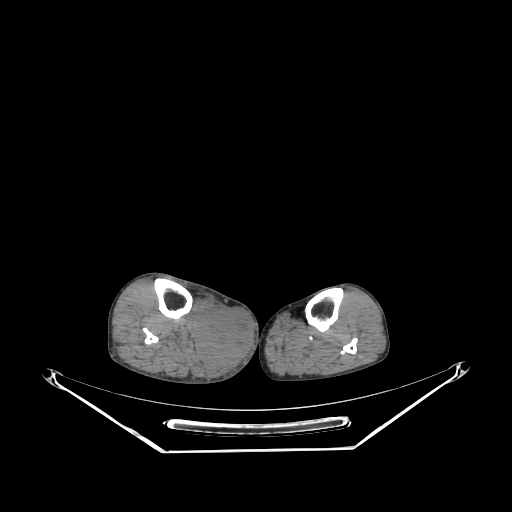
CT of an extremity soft-tissue mass (from a PET/CT study), one axial slice; slice 138 of 267 in the series (ordered by position); 140 kVp; soft-tissue window (W 400 / L 40 HU); 3.75 mm slice thickness; 512 × 512 image matrix, field of view 500 × 500 mm. Male patient. From the clinical record (not read from this slice): histological type: pleiomorphic liposarcoma; grade: high; site of the primary tumour: right calf.
Annotated regions visible in this slice (expert contour drawn on MRI and transferred to this co-registered scan by the dataset authors):
- gross tumour volume including surrounding oedema: box from (x=194, y=306) to (x=252, y=369) px
- gross tumour volume (mass): (x=194, y=306)–(x=252, y=366)